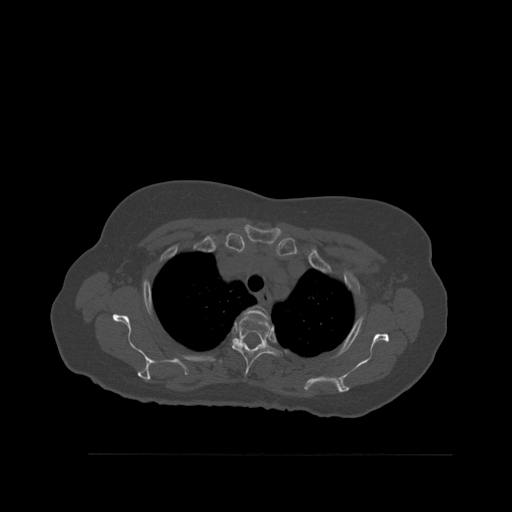
CT including the spine, one axial slice. Slice 420 of 527 in the series (ordered by position). Bone window (W 1800 / L 400 HU). 1.5 mm slice thickness. 512 × 512 image matrix. Patient: female, 73 years. Case-level facts recorded for this patient, not image findings: primary cancer: breast; vertebrae with lytic lesions (as recorded): L2.
Annotated regions visible in this slice (semi-automatically segmented with operator editing):
- T2 vertebra: box from (x=244, y=306) to (x=270, y=320) px
- T3 vertebra: (x=230, y=313)–(x=278, y=381)
- T4 vertebra: (x=219, y=359)–(x=223, y=364)